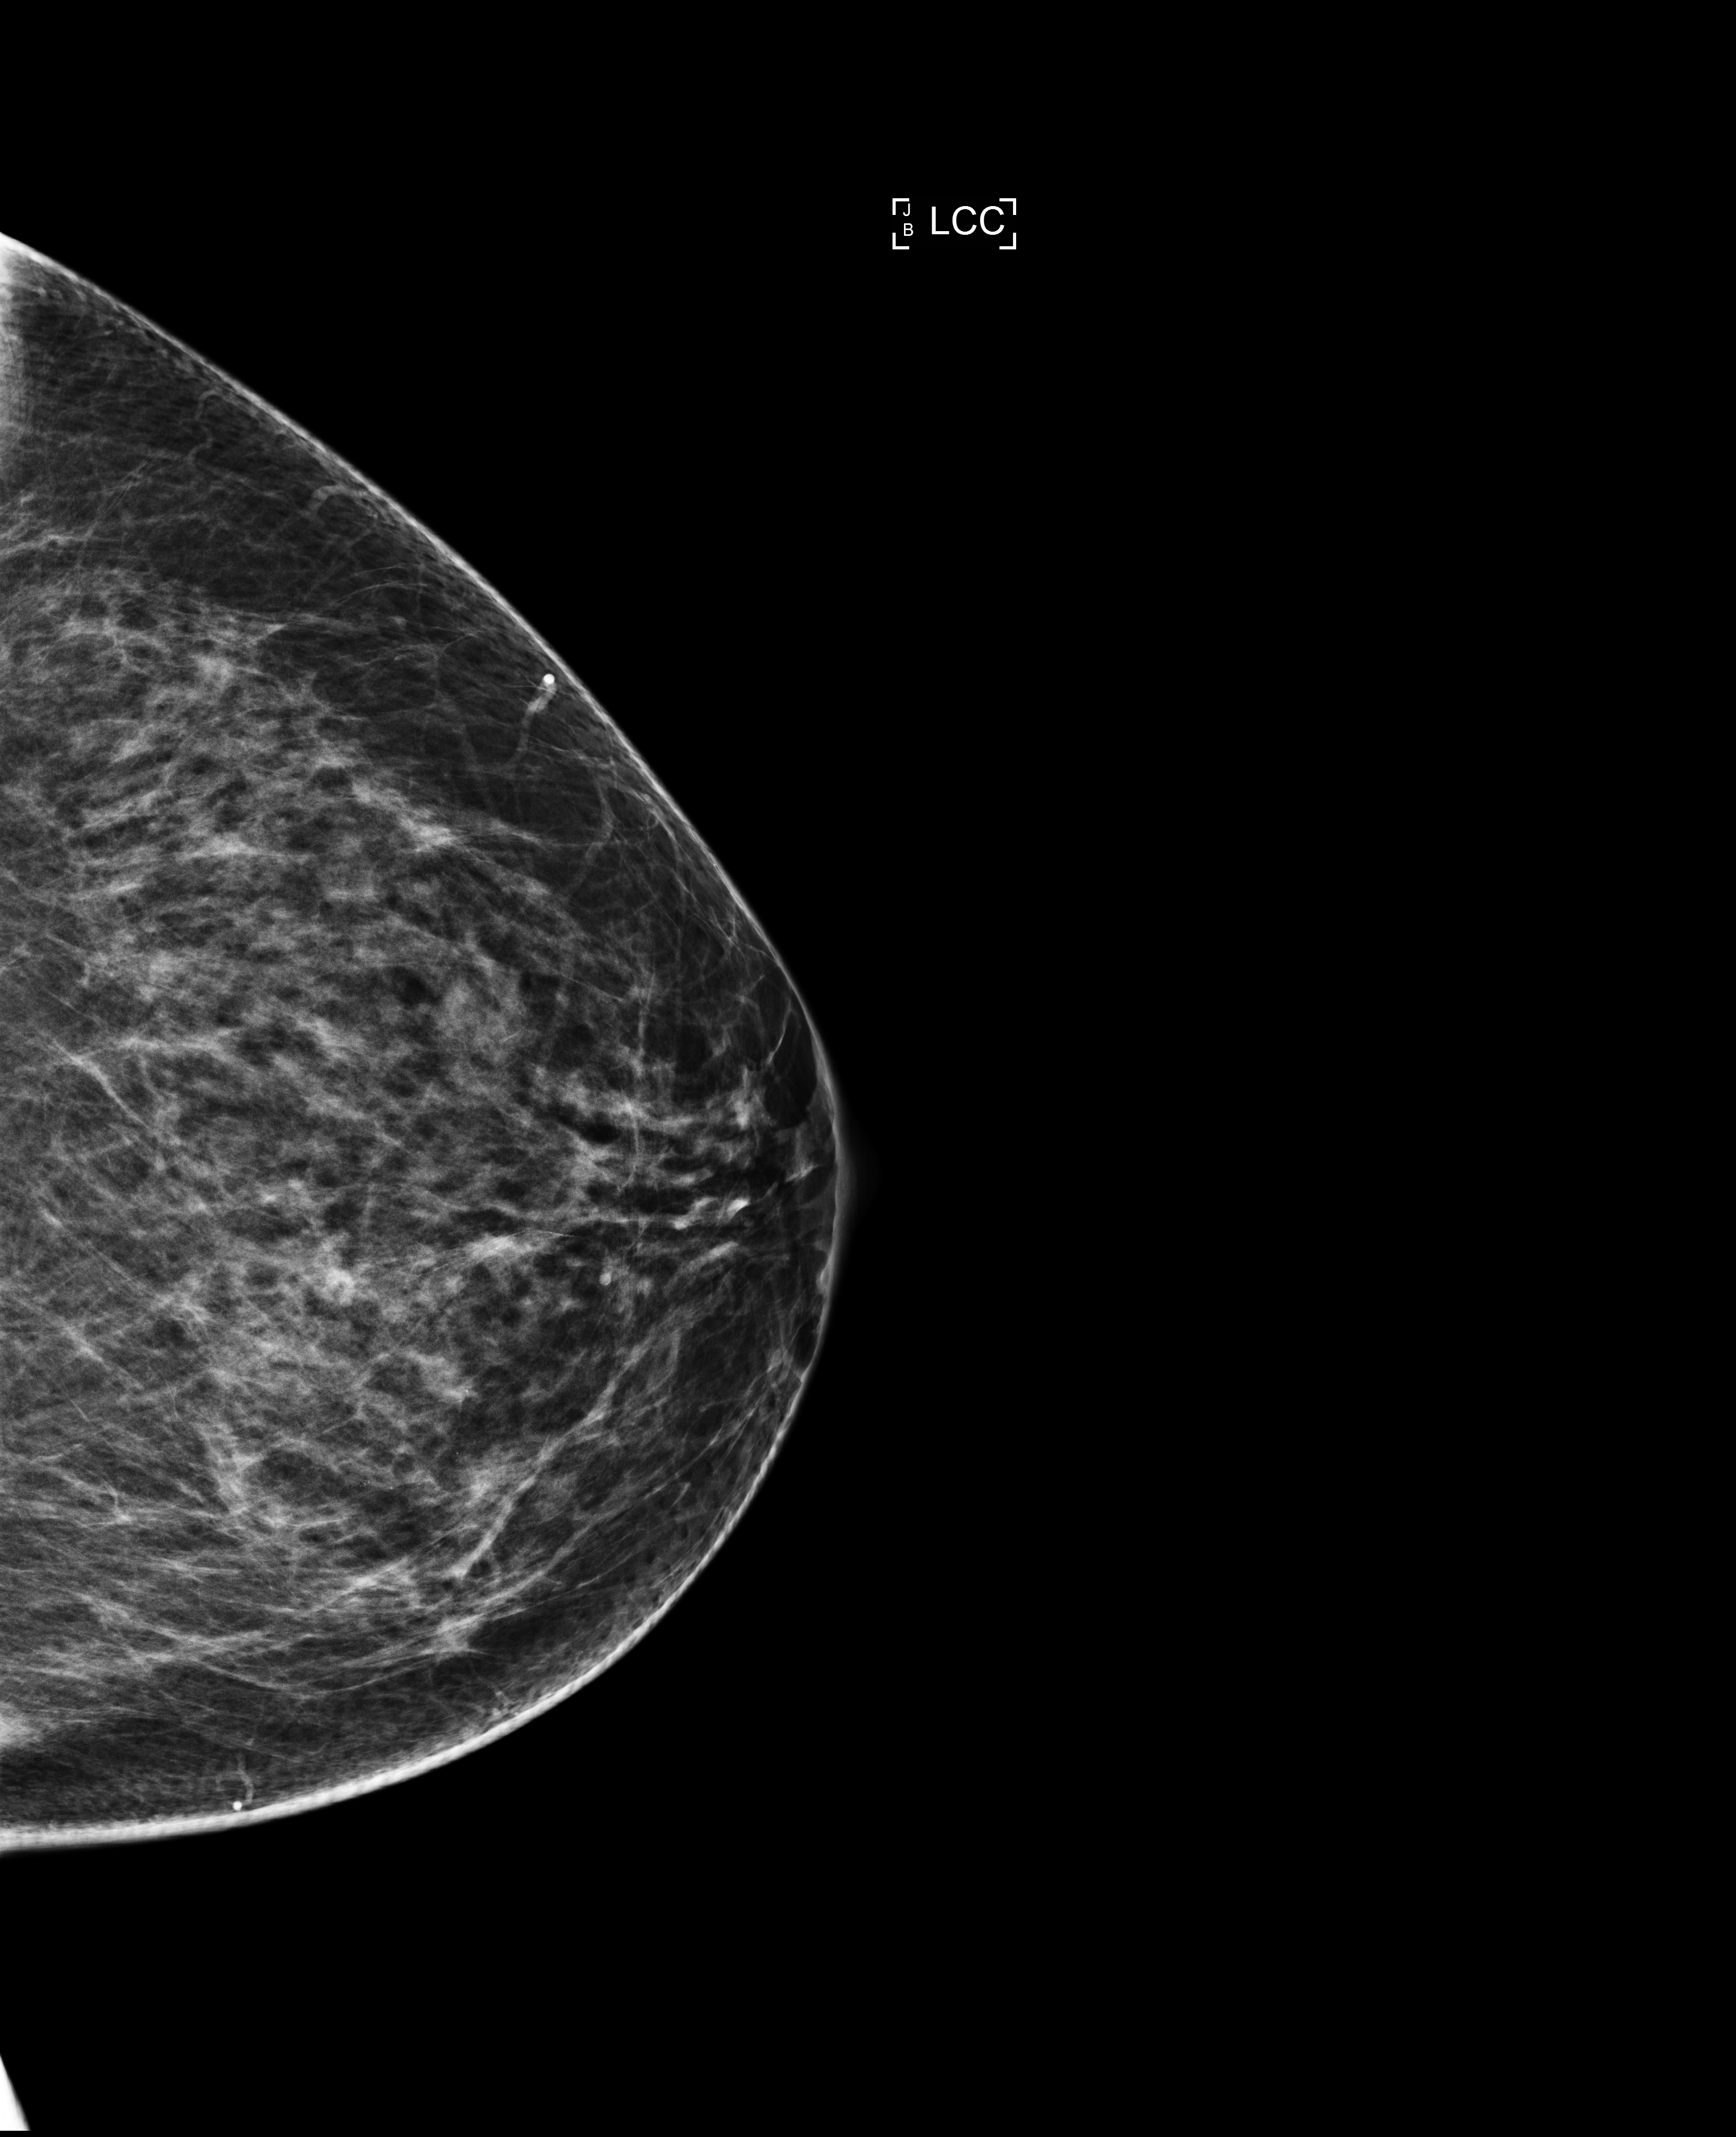
Screening examination, compressed breast thickness 78 mm.
Image type: full-field digital mammogram. Breast: left. Projection: craniocaudal (CC) view.